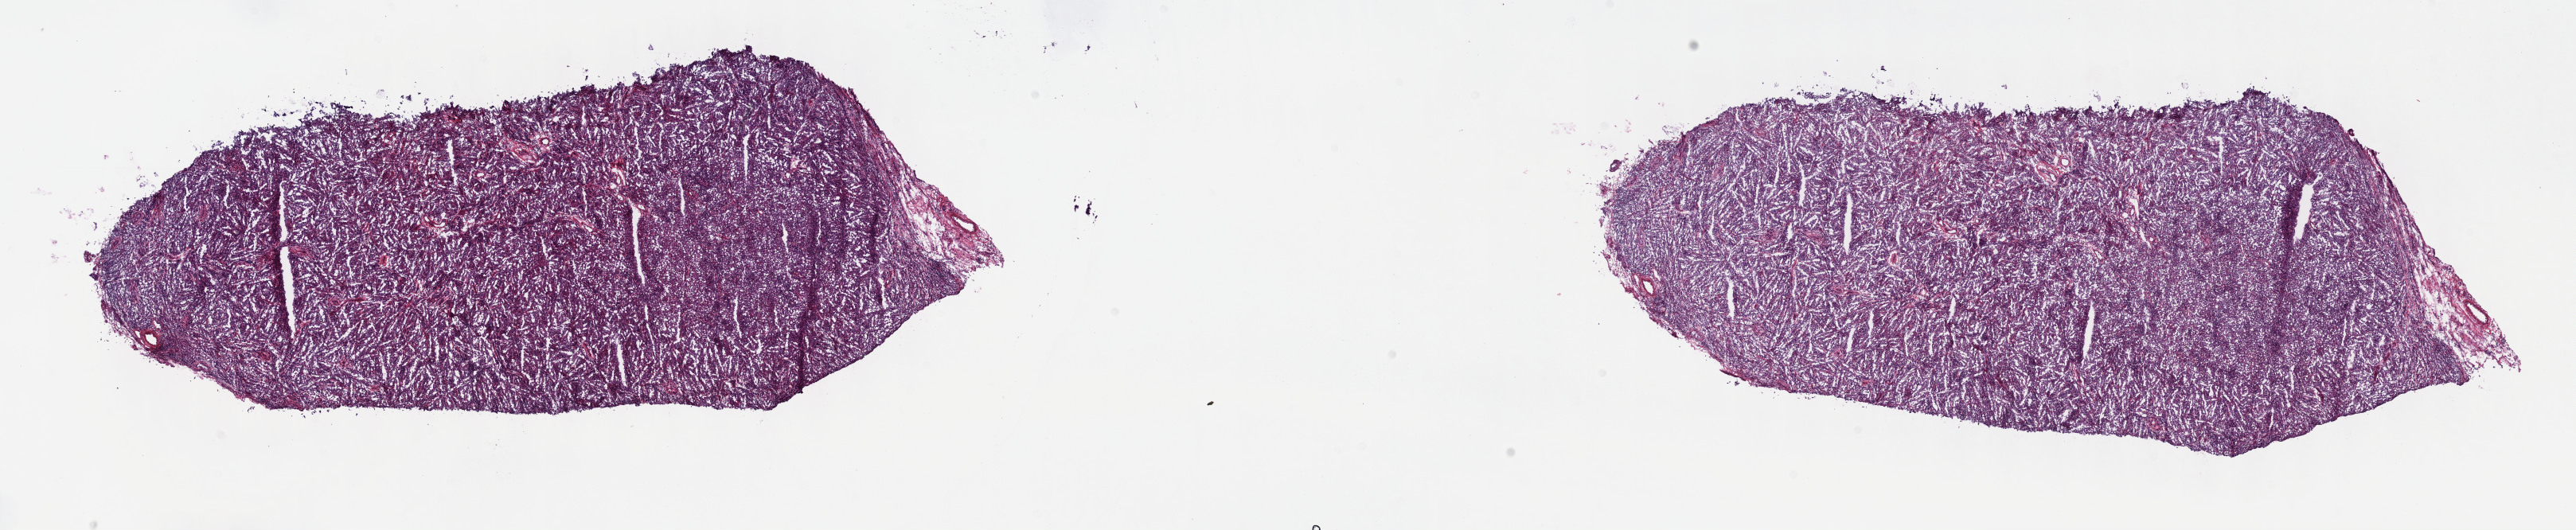
Whole-slide histology image, H&E-stained, whole scanned area (about 26.2 x 5.4 mm, slide scanned at 40x) shown as a low-resolution overview; frozen section from the top of the tissue portion; testis, primary tumour sample. Male, age 33 years at initial diagnosis. Slide review estimates, as recorded: tumour cells 100%, tumour nuclei 80%, normal cells 0%, stromal cells 0%, necrosis 0%. Inflammatory infiltration, as recorded: lymphocyte infiltration 2%, monocyte infiltration 0%, neutrophil infiltration 0%.
AJCC pathologic stage: IS (5th edition). Pathologic diagnosis: Seminoma, NOS. Laterality: left.